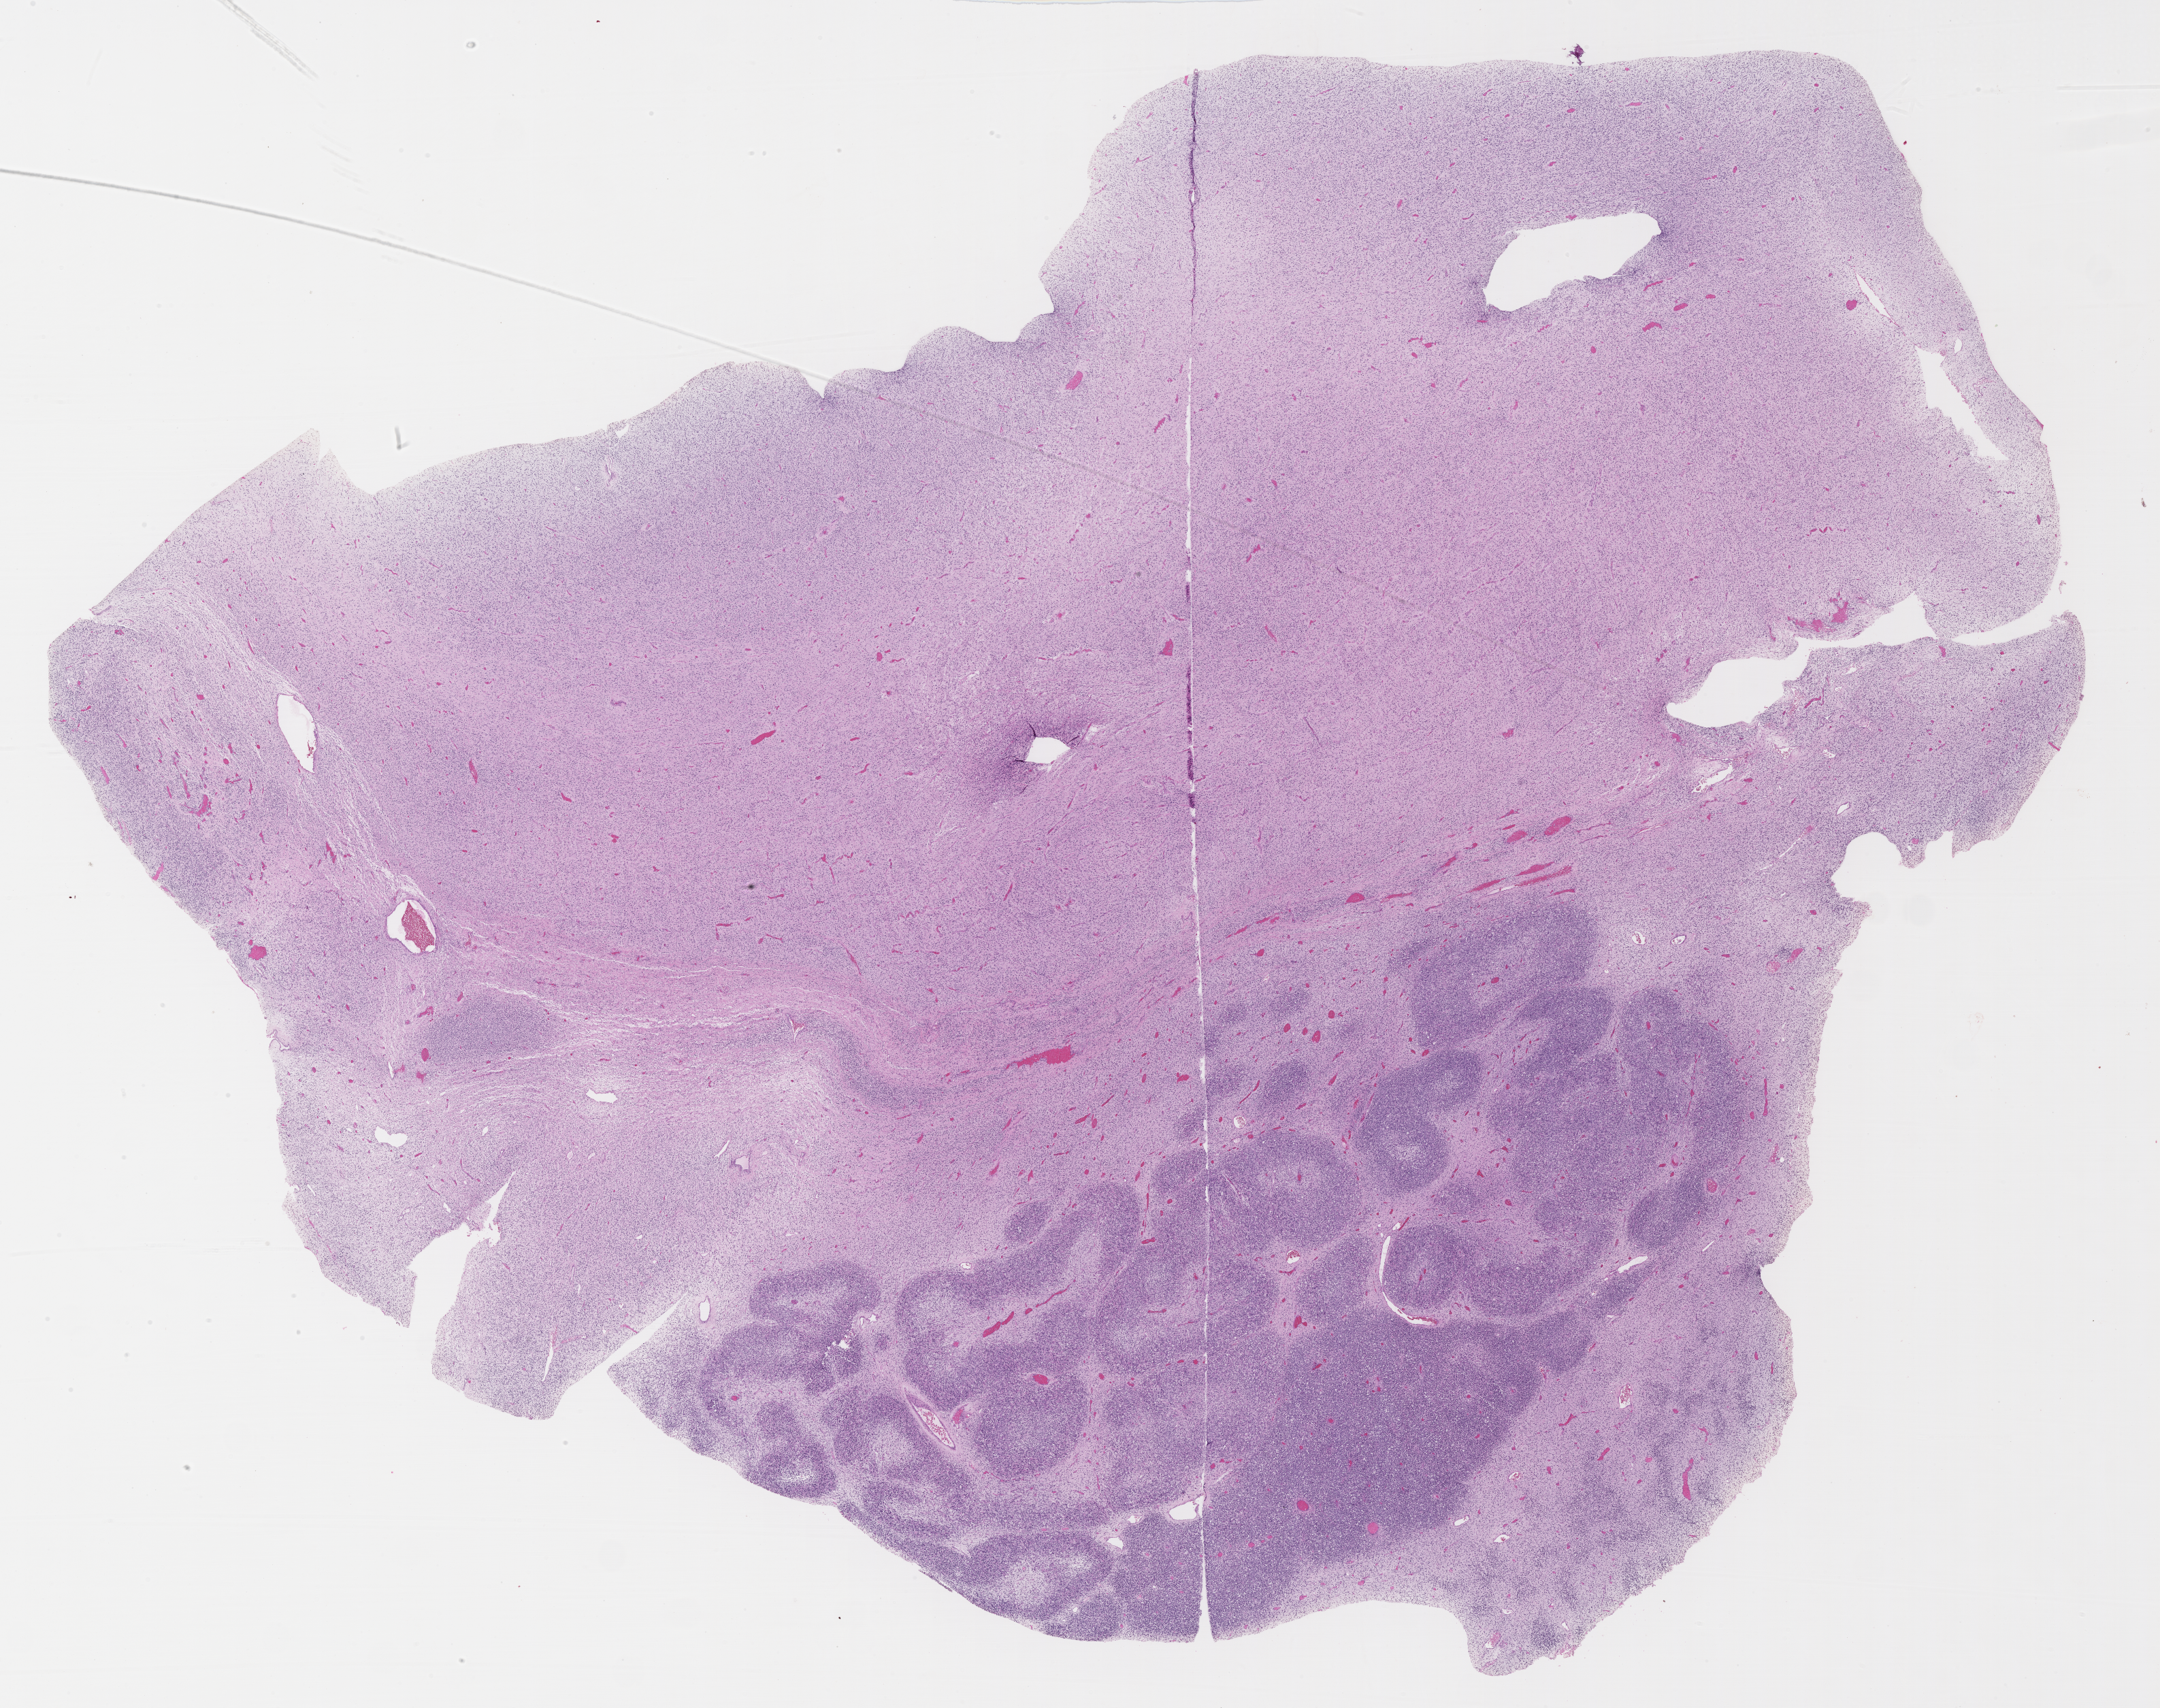
Digitized haematoxylin and eosin-stained section of tumor tissue — a low-resolution overview of the entire scanned area, about 25.7 x 20.3 mm; formalin-fixed, paraffin-embedded (FFPE) tissue; site: paratesticular, left. Patient: male, age 14.3 years at diagnosis.
Stage (as recorded): 4. Metastatic status at presentation (as recorded): metastatic (confirmed). Diagnosis: rhabdomyosarcoma; histological classification: embryonal rhabdomyosarcoma. Primary site (case record): testis-paratesticular.